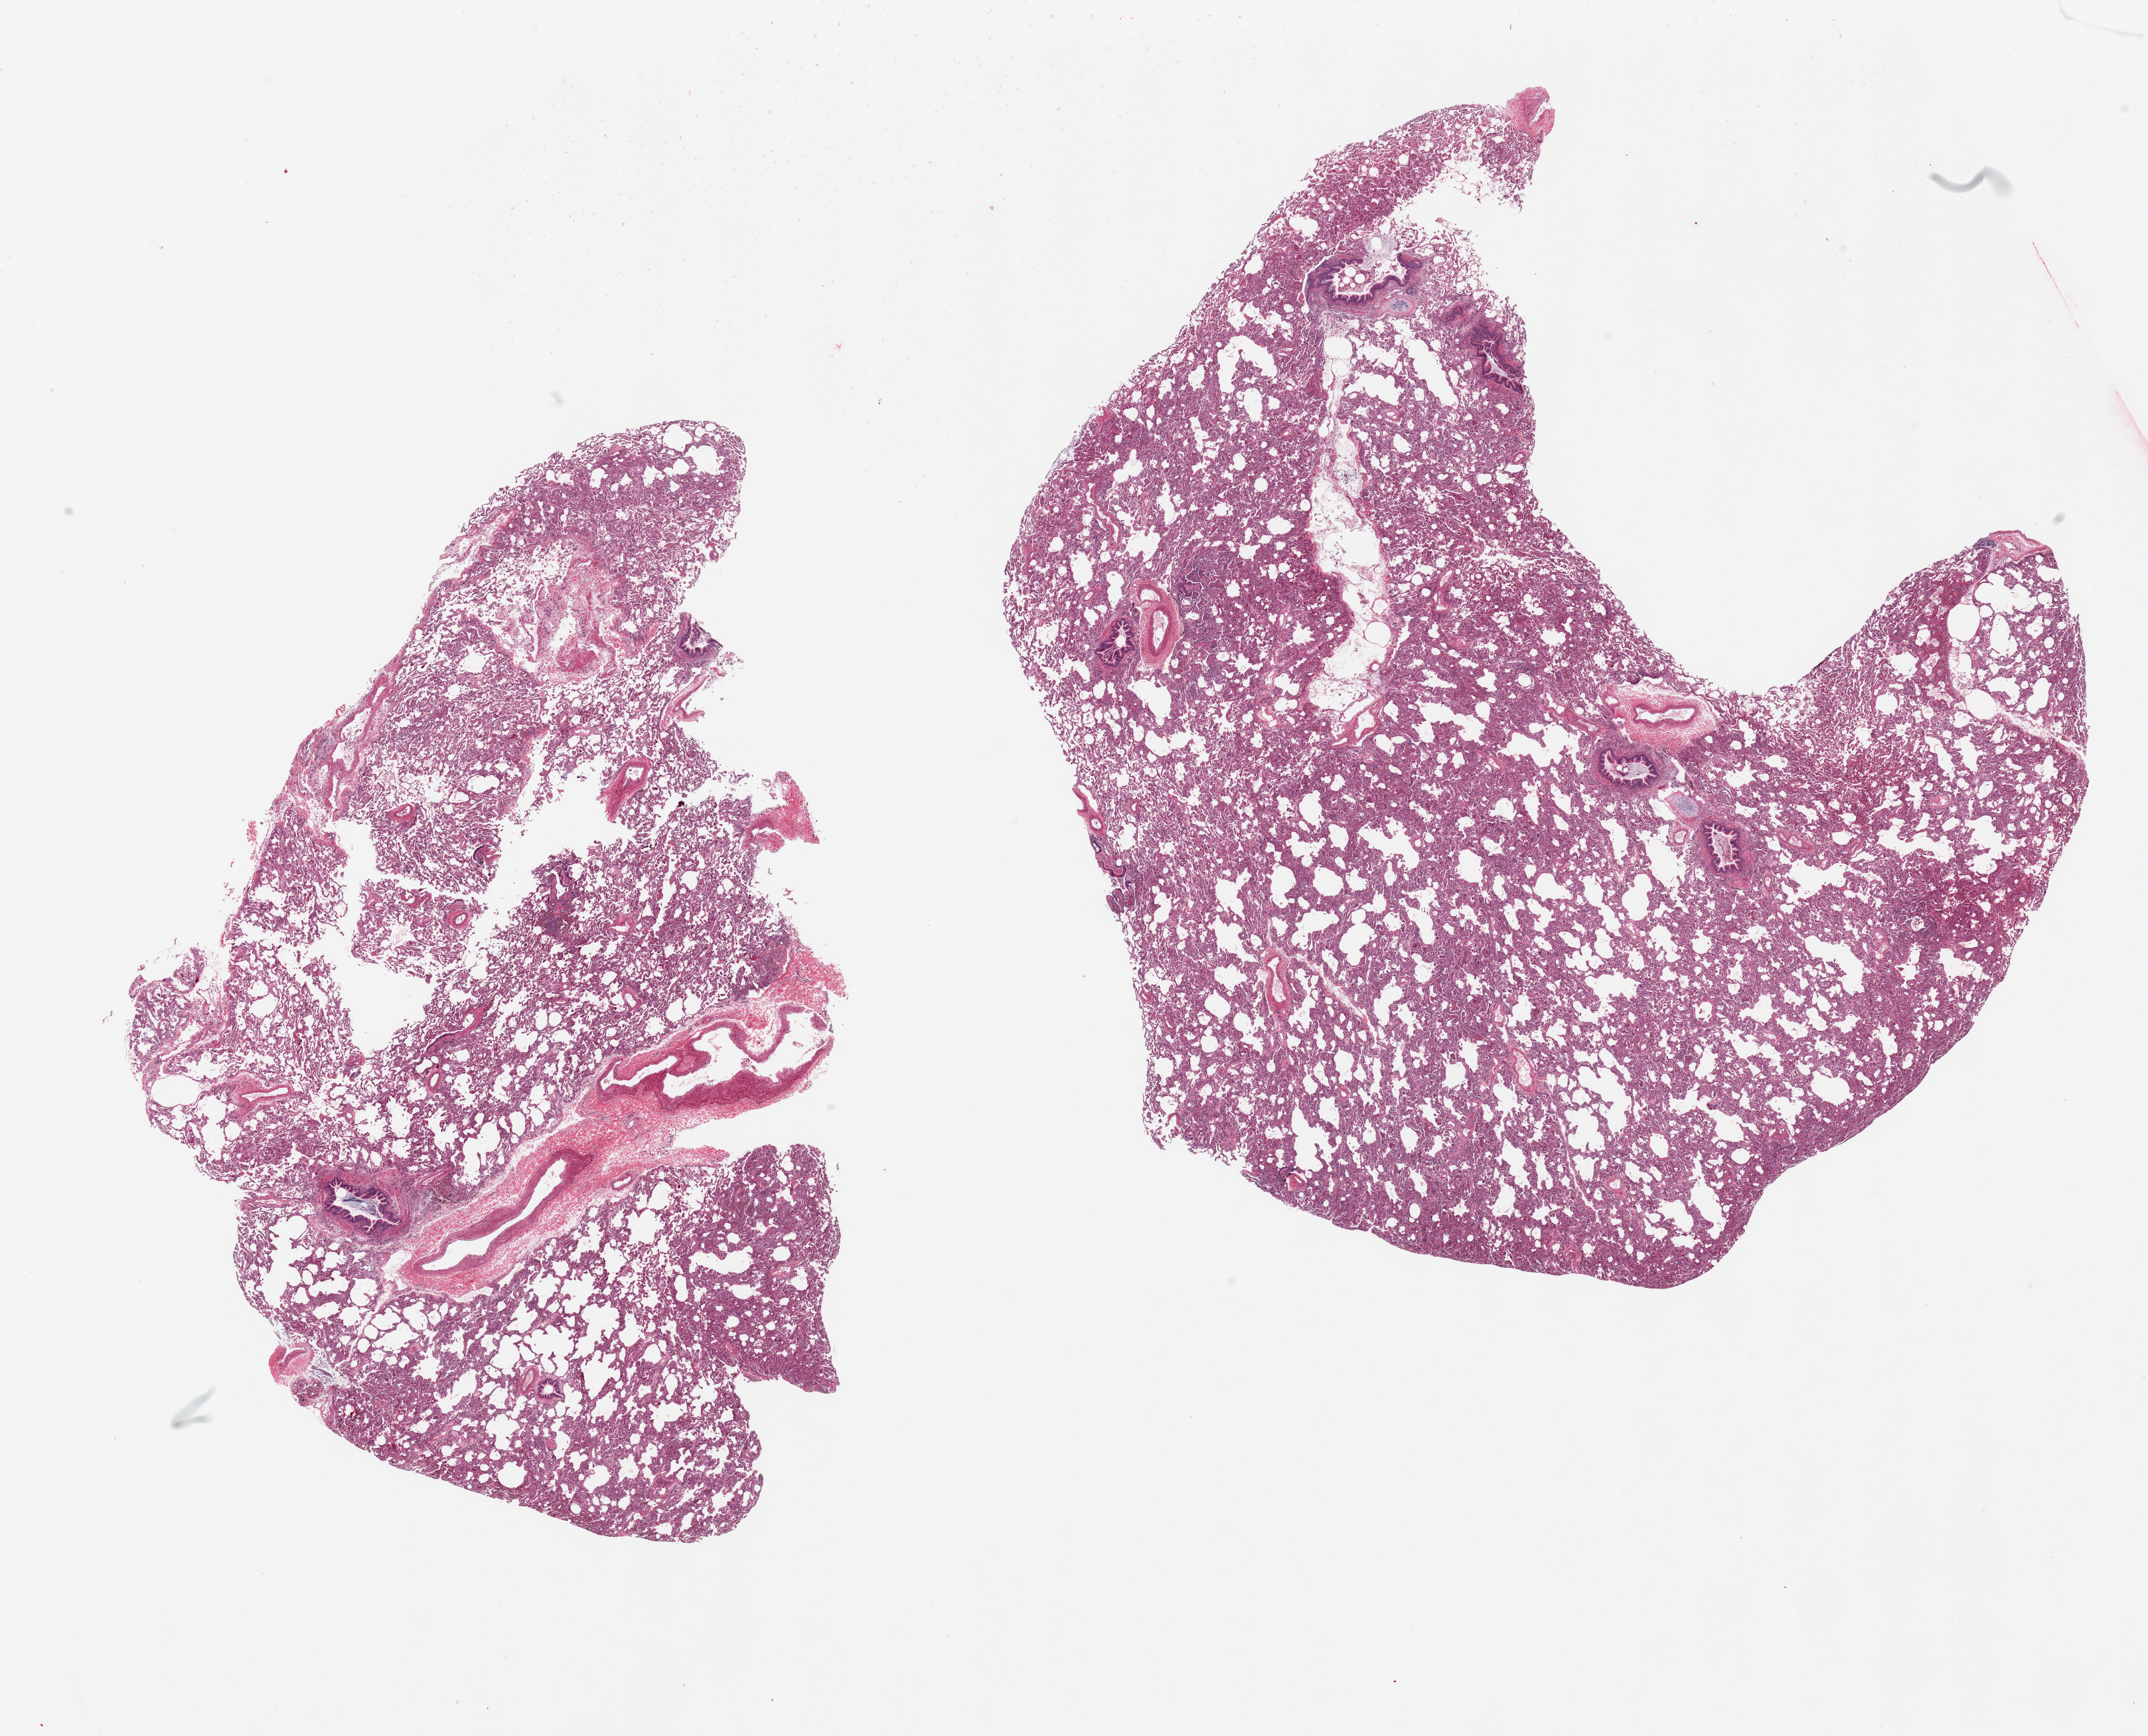
H&E whole-slide image, low-resolution overview of the scanned area, about 25.6 x 20.7 mm (slide scanned at 20x). PAXgene-fixed paraffin-embedded (PFPE) section. Sampled site (target tissue): lung. Donor tissue sample. Donor sex: male.
• reviewer comment on this tissue sample: 2 pieces